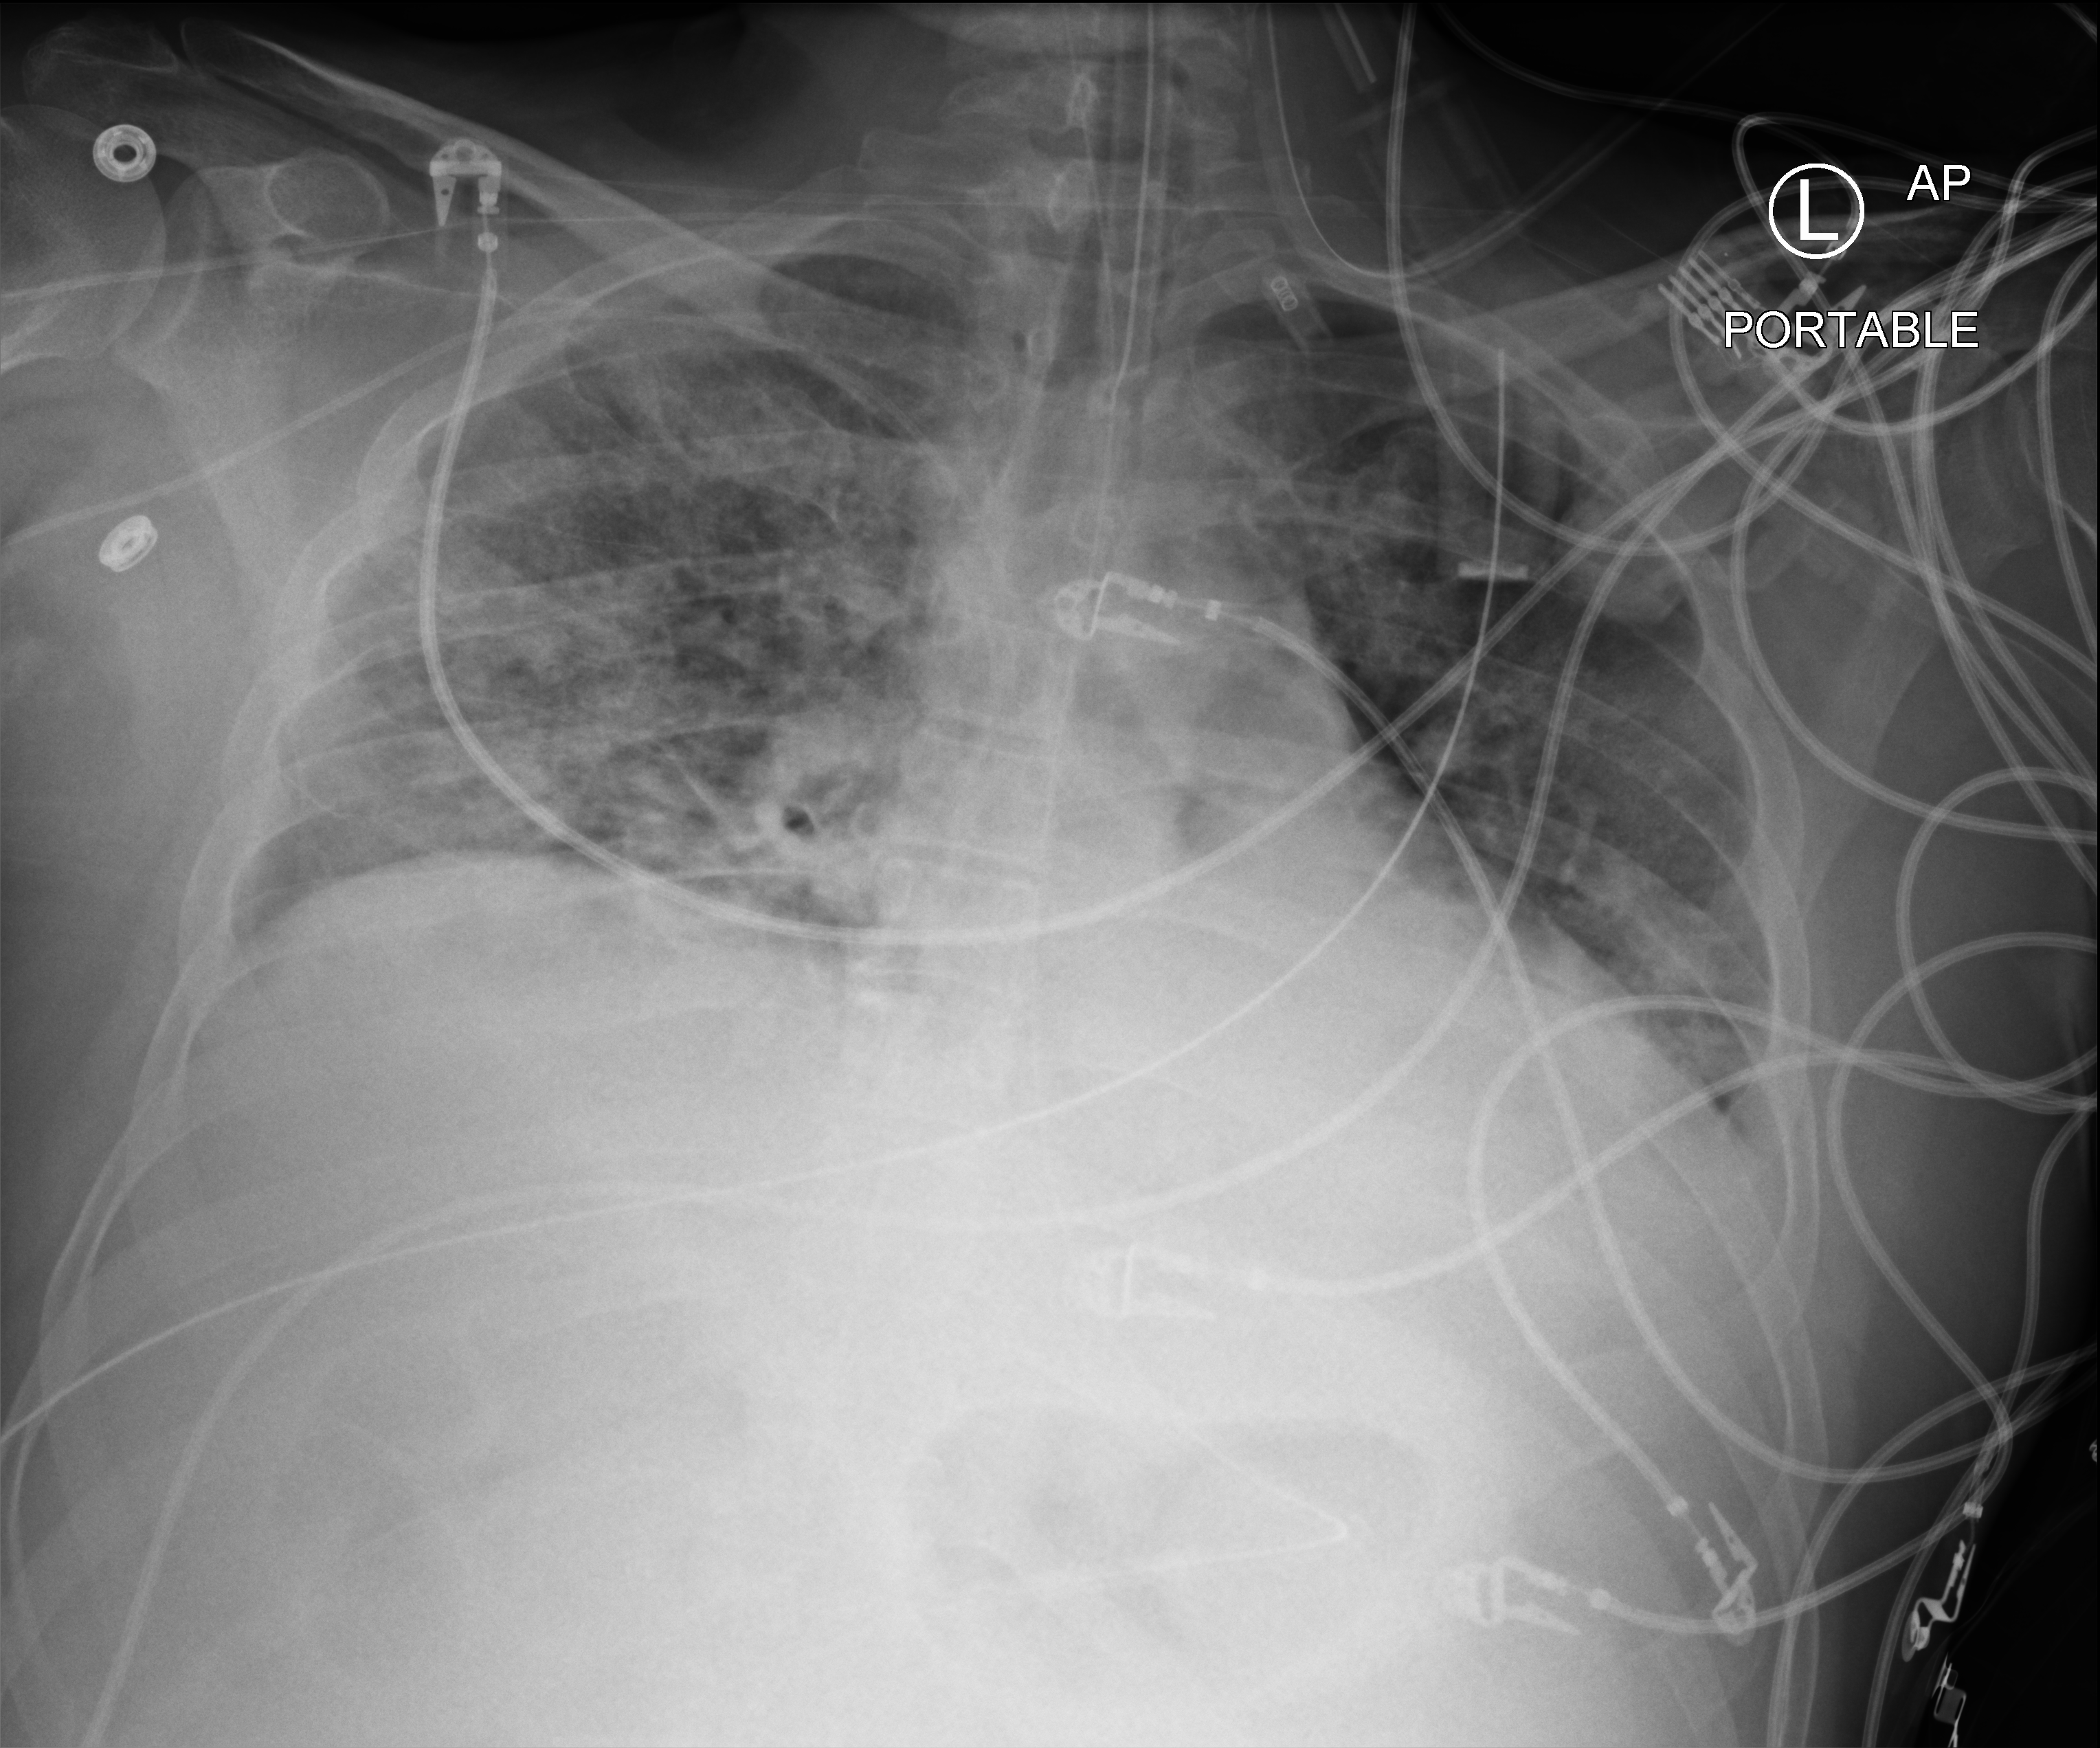
Portable chest radiograph, anteroposterior (AP) projection. Male patient hospitalised with COVID-19, age 18–59 years.
Hospital-stay facts (about this admission, not read from this image; timing relative to this image not recorded):
- length of hospital stay: 48 days
- smoking status (admission record): never
- admitted to intensive care during this hospital stay: yes